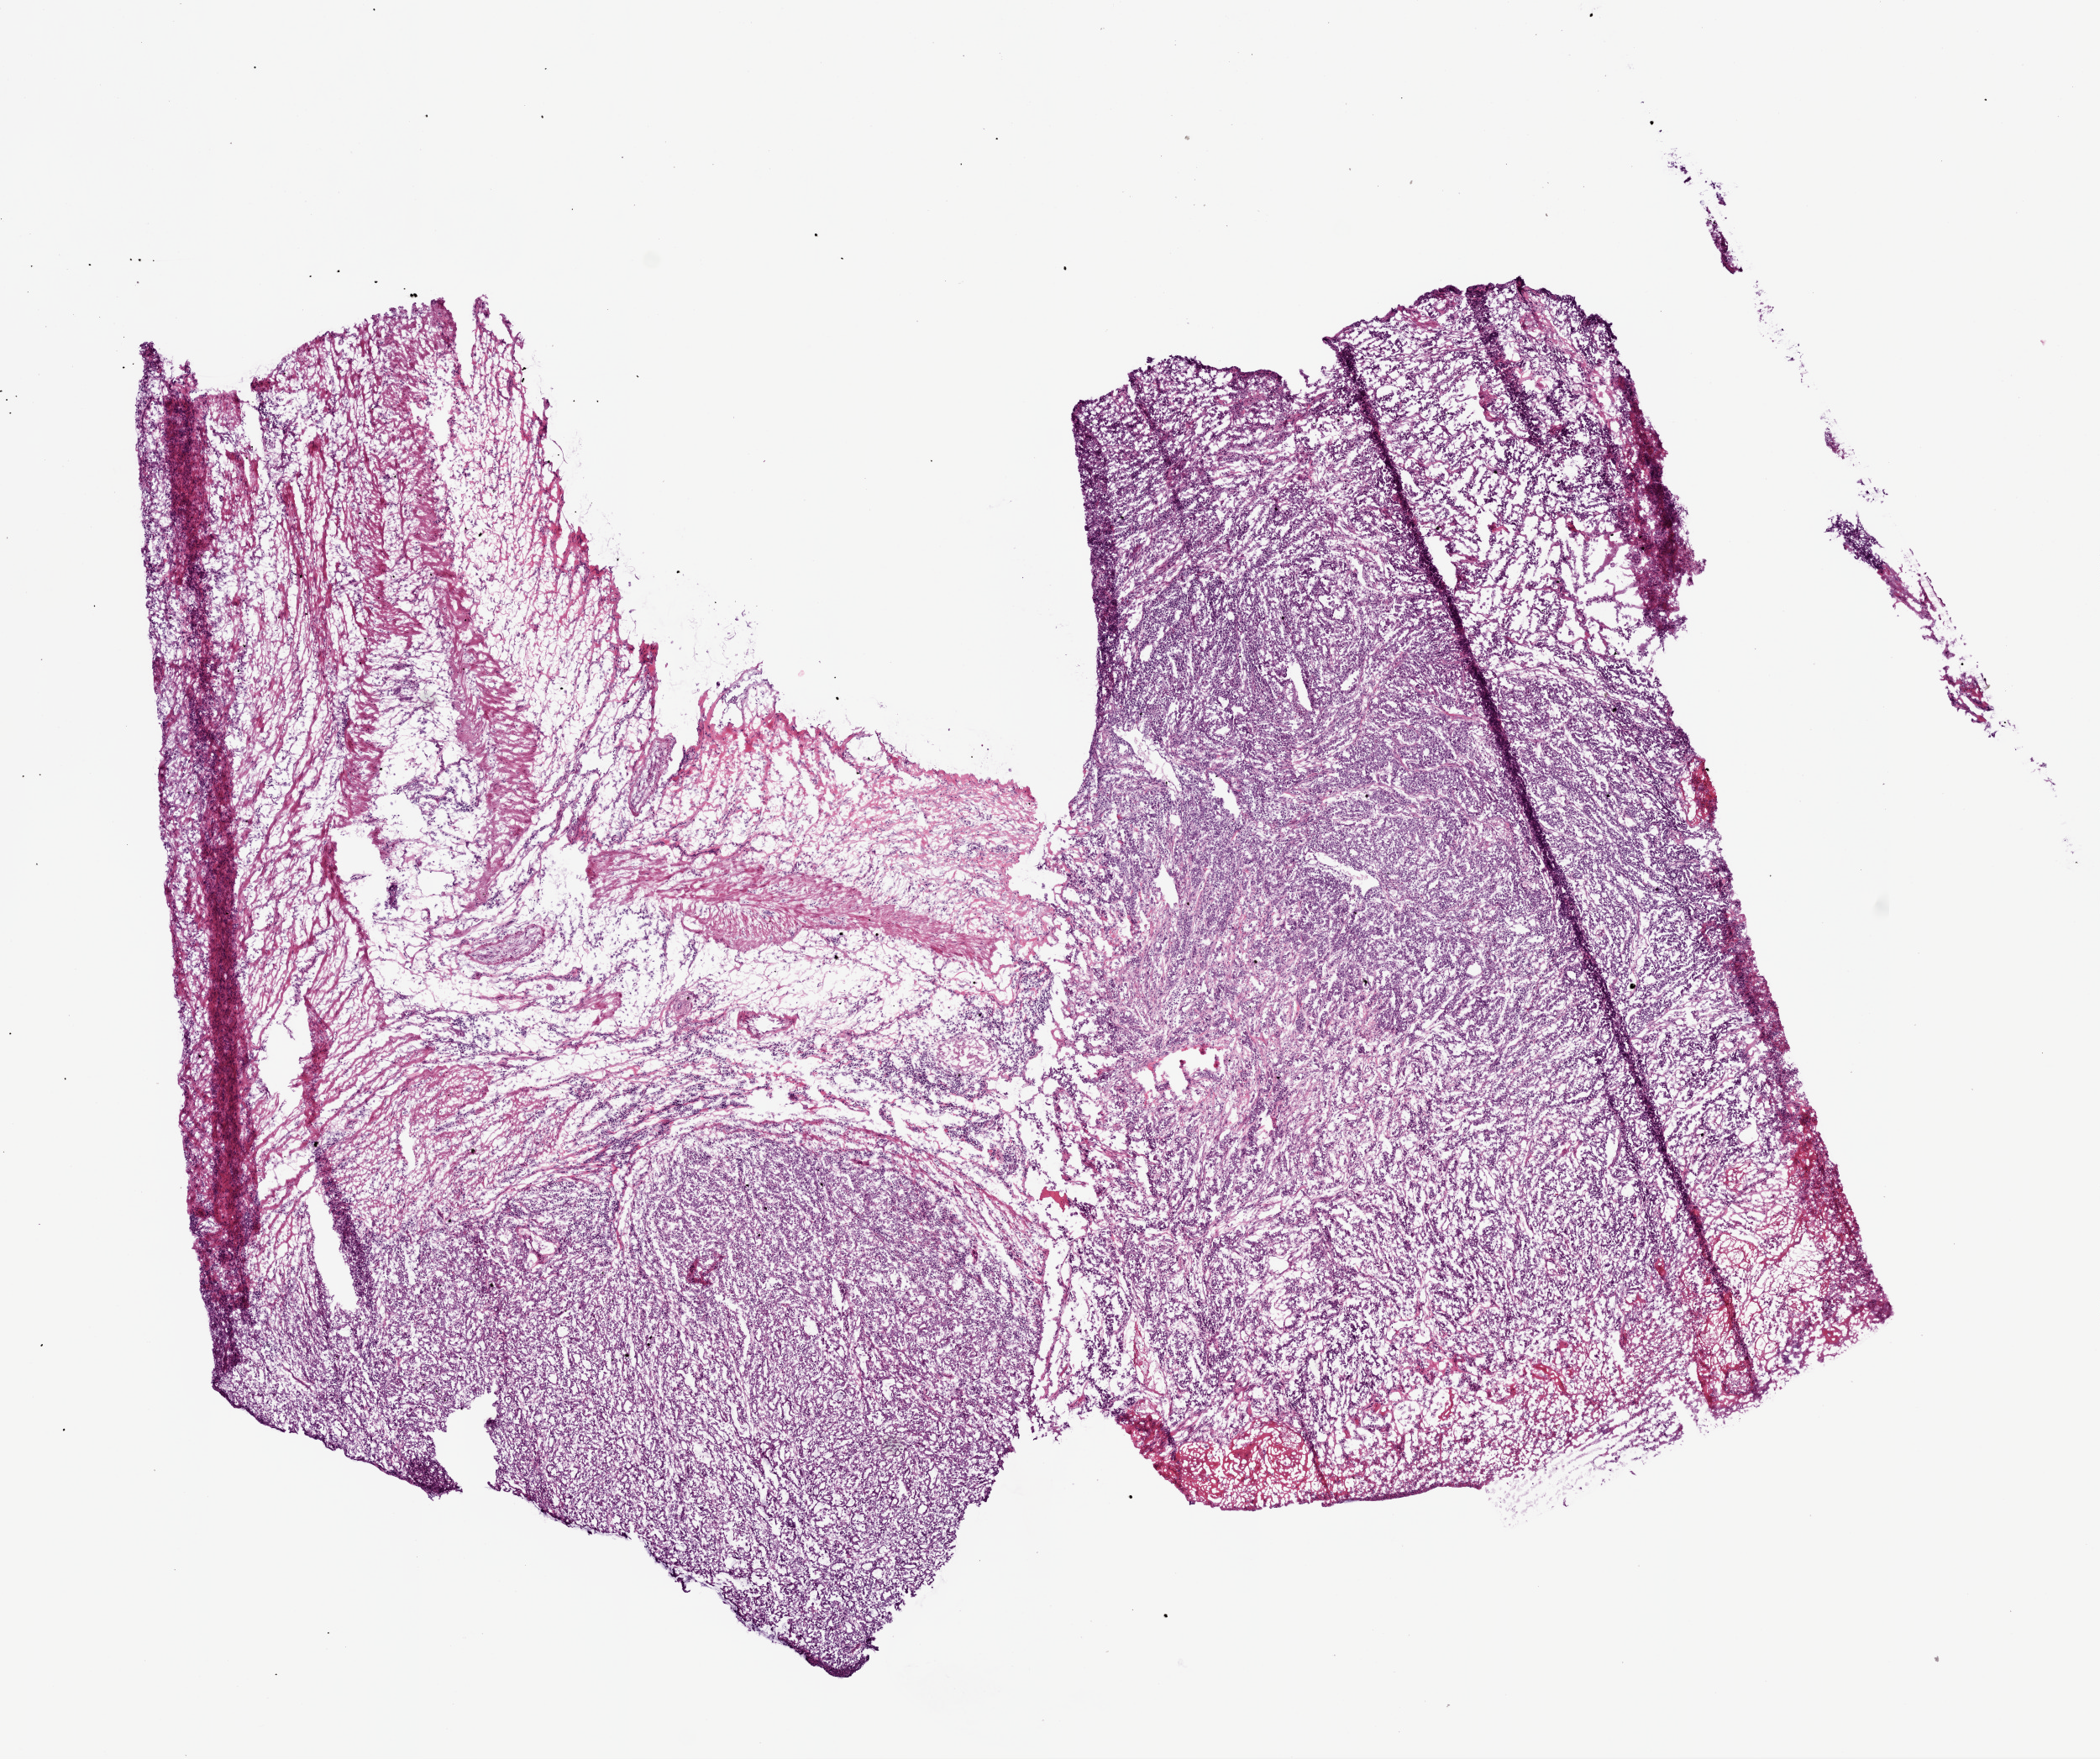
Whole-slide histology image, Hematoxylin and eosin (H&E) stained — shown as a low-resolution overview of the whole scanned area (about 10.0 x 8.4 mm); frozen section from the bottom of the tissue portion; sample: primary tumour, stomach. Male patient. Histologic grade: G3 (poorly differentiated). Composition of this section per pathologist review: tumour cells 55%, tumour nuclei 75%, normal cells 0%, stromal cells 40%, necrosis 5%.
Pathologic diagnosis: Adenocarcinoma, NOS (cardia, NOS). AJCC pathologic stage: II (5th edition).